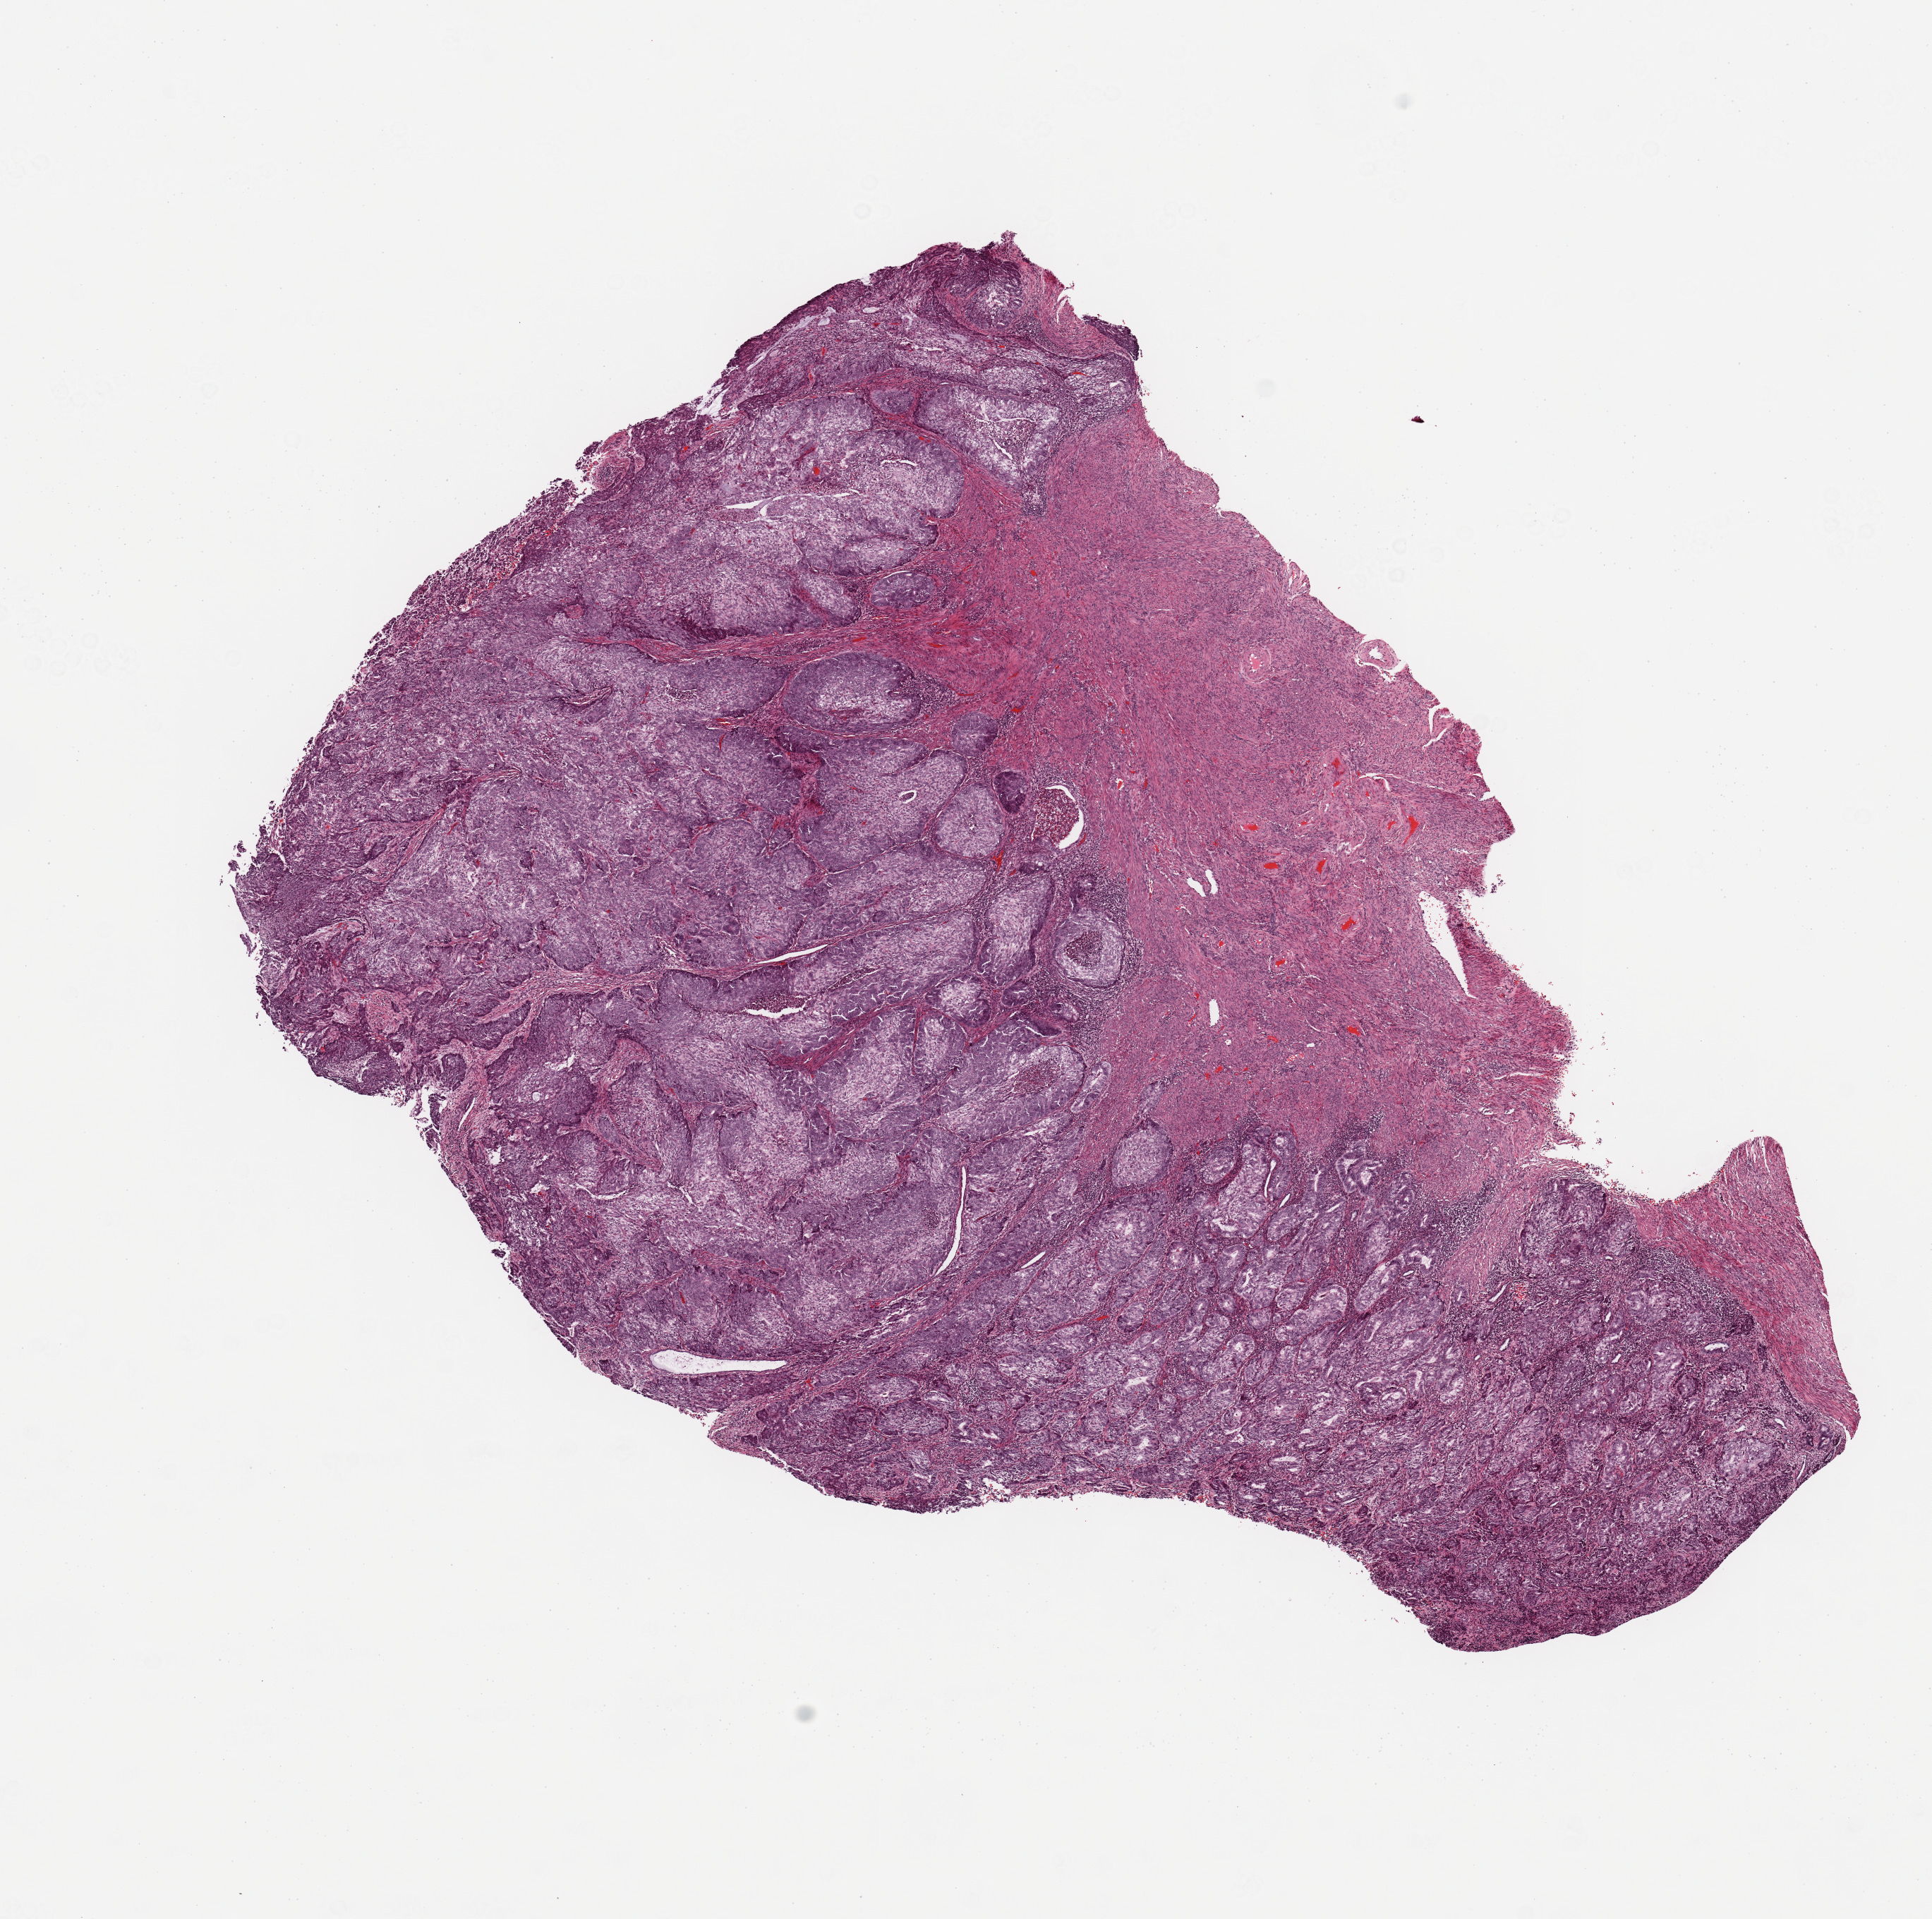
Whole-slide histology image, H&E — whole scanned area (about 10.8 x 10.8 mm, acquisition: 20x scan) shown as a low-resolution overview; tumour tissue sample, sampled site: uterus. Patient: female, age 64 years. Histologic grade: G3 (poorly differentiated). Slide review estimates, as recorded: tumour nuclei 80%, necrosis 5%.
• diagnosis: Endometrioid adenocarcinoma, NOS
• AJCC pathologic stage: I
• primary tumour site (as recorded): anterior endometrium